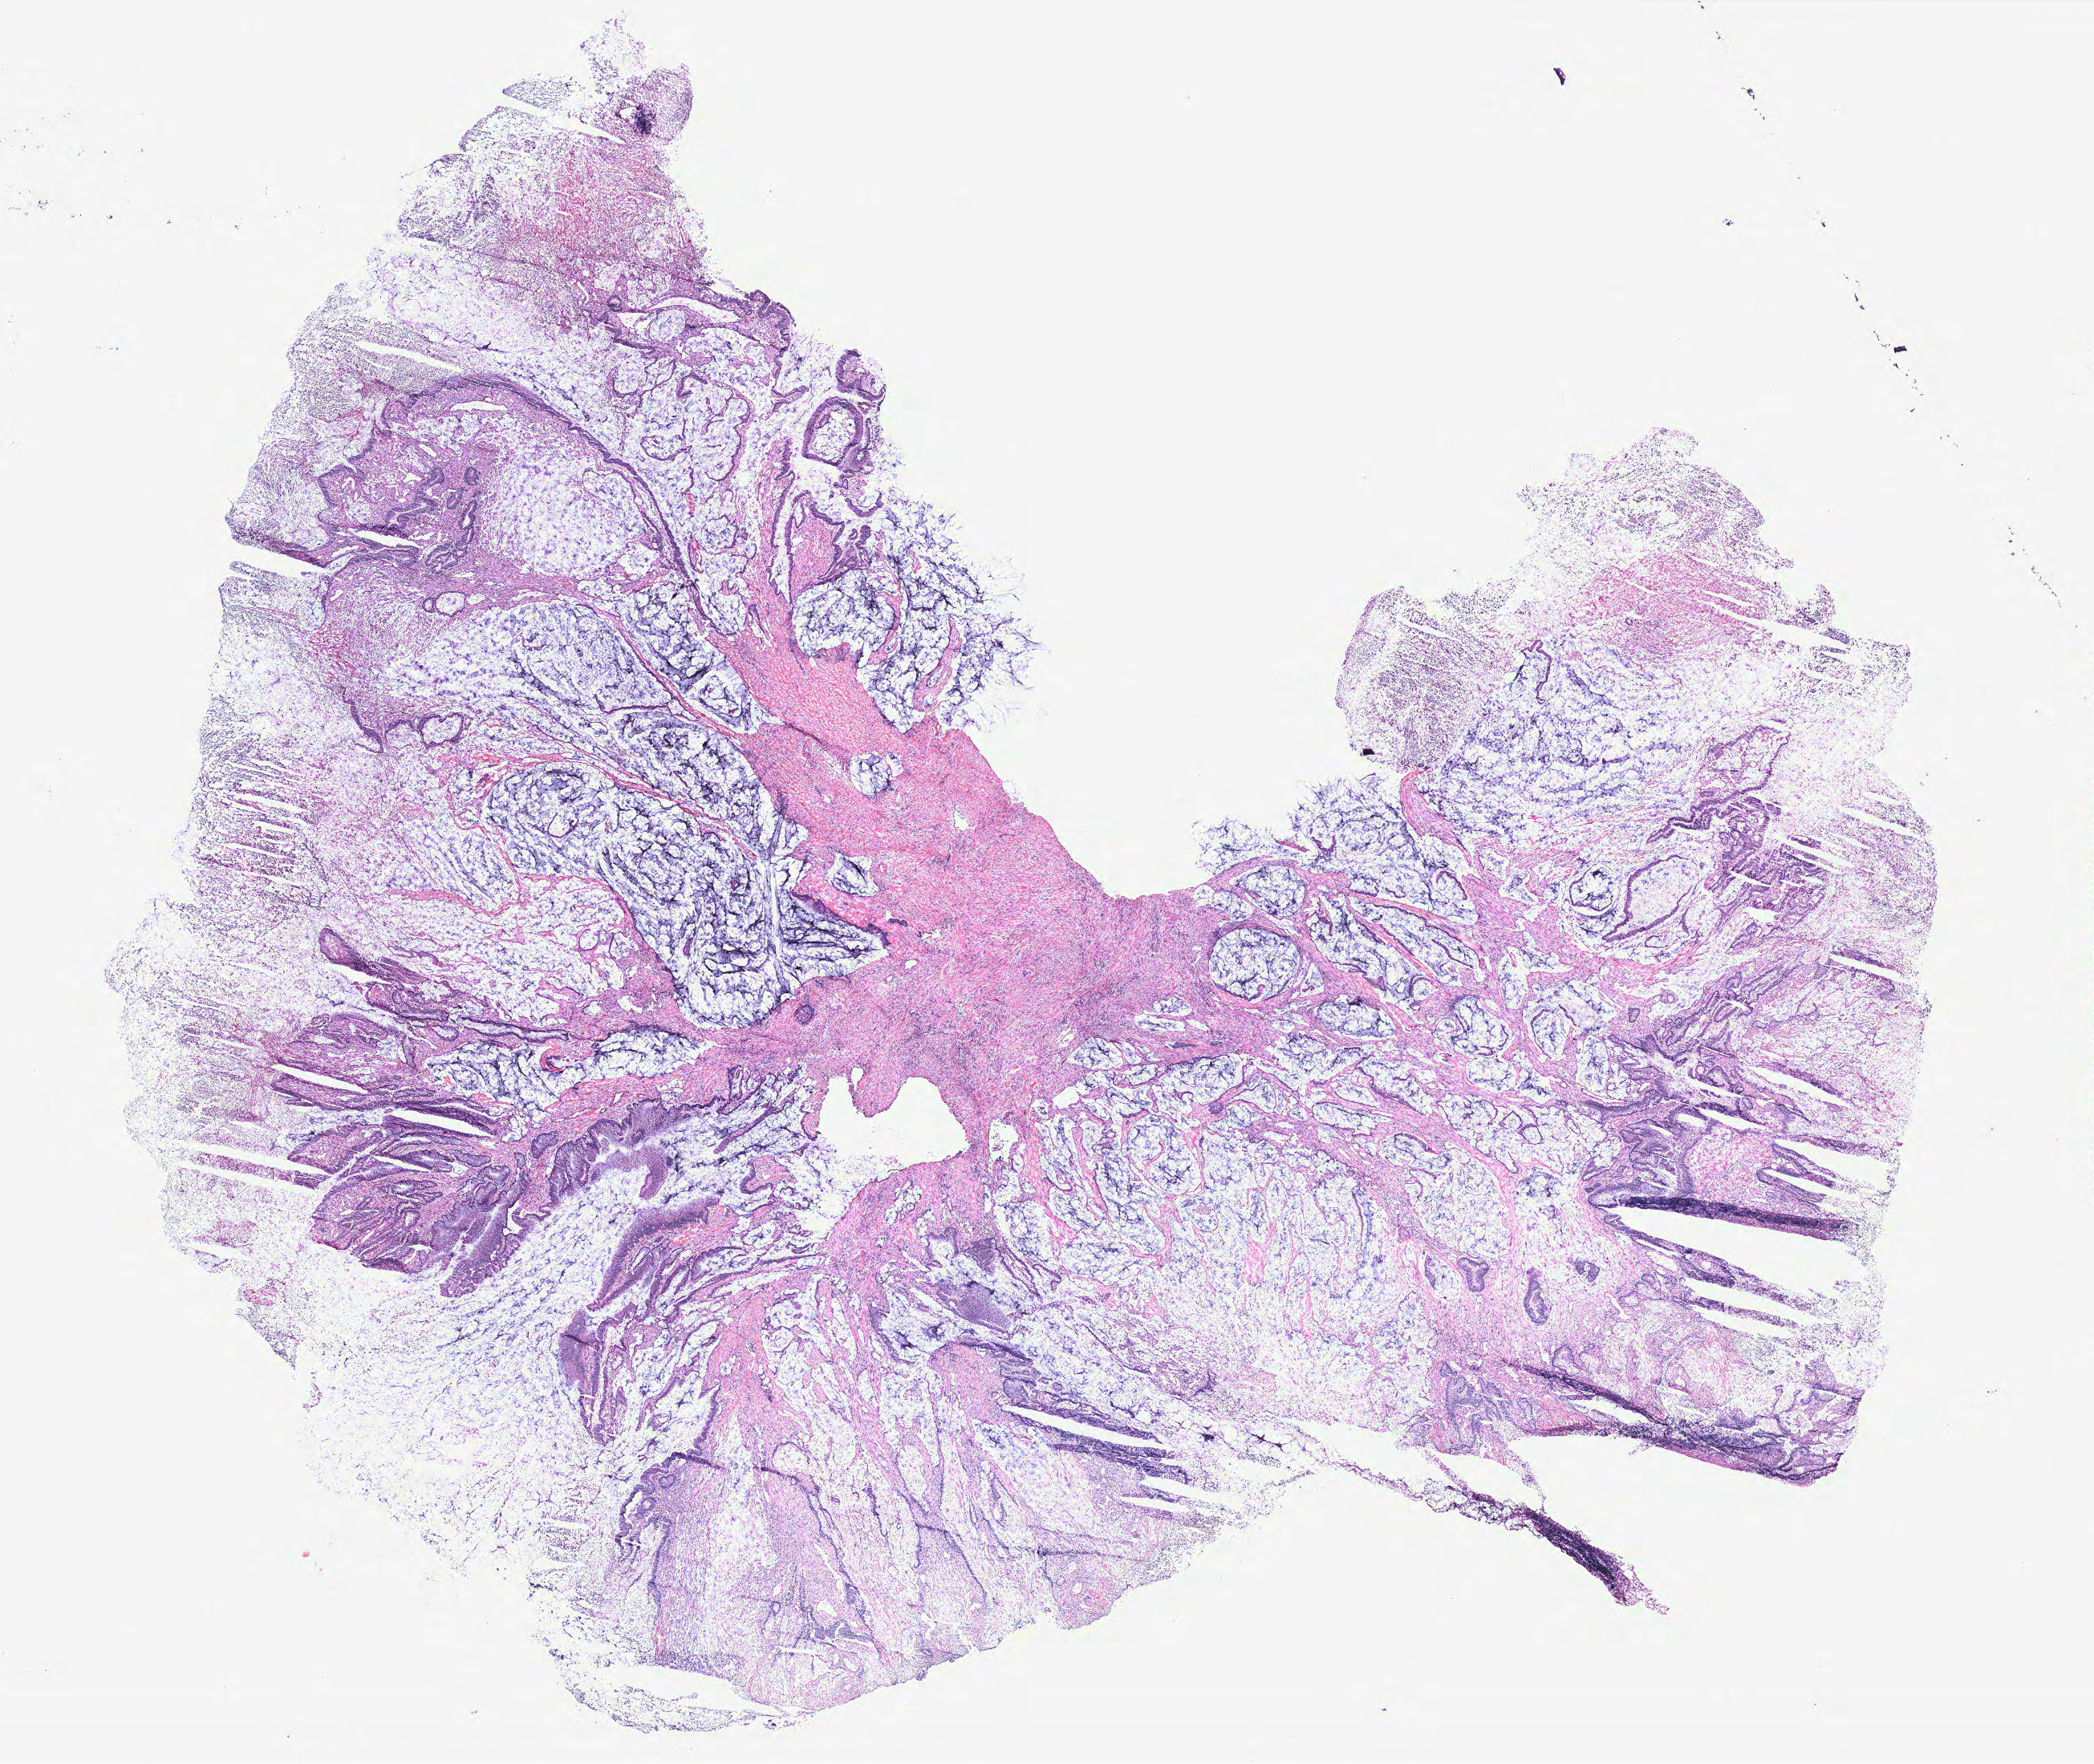
Hematoxylin and eosin (H&E) stained whole-slide image — shown as a low-resolution overview of the whole scanned area (about 20.9 x 17.6 mm). Colon, tissue type not recorded.
* patient diagnosis (cohort enrolment): colon cancer (colon)